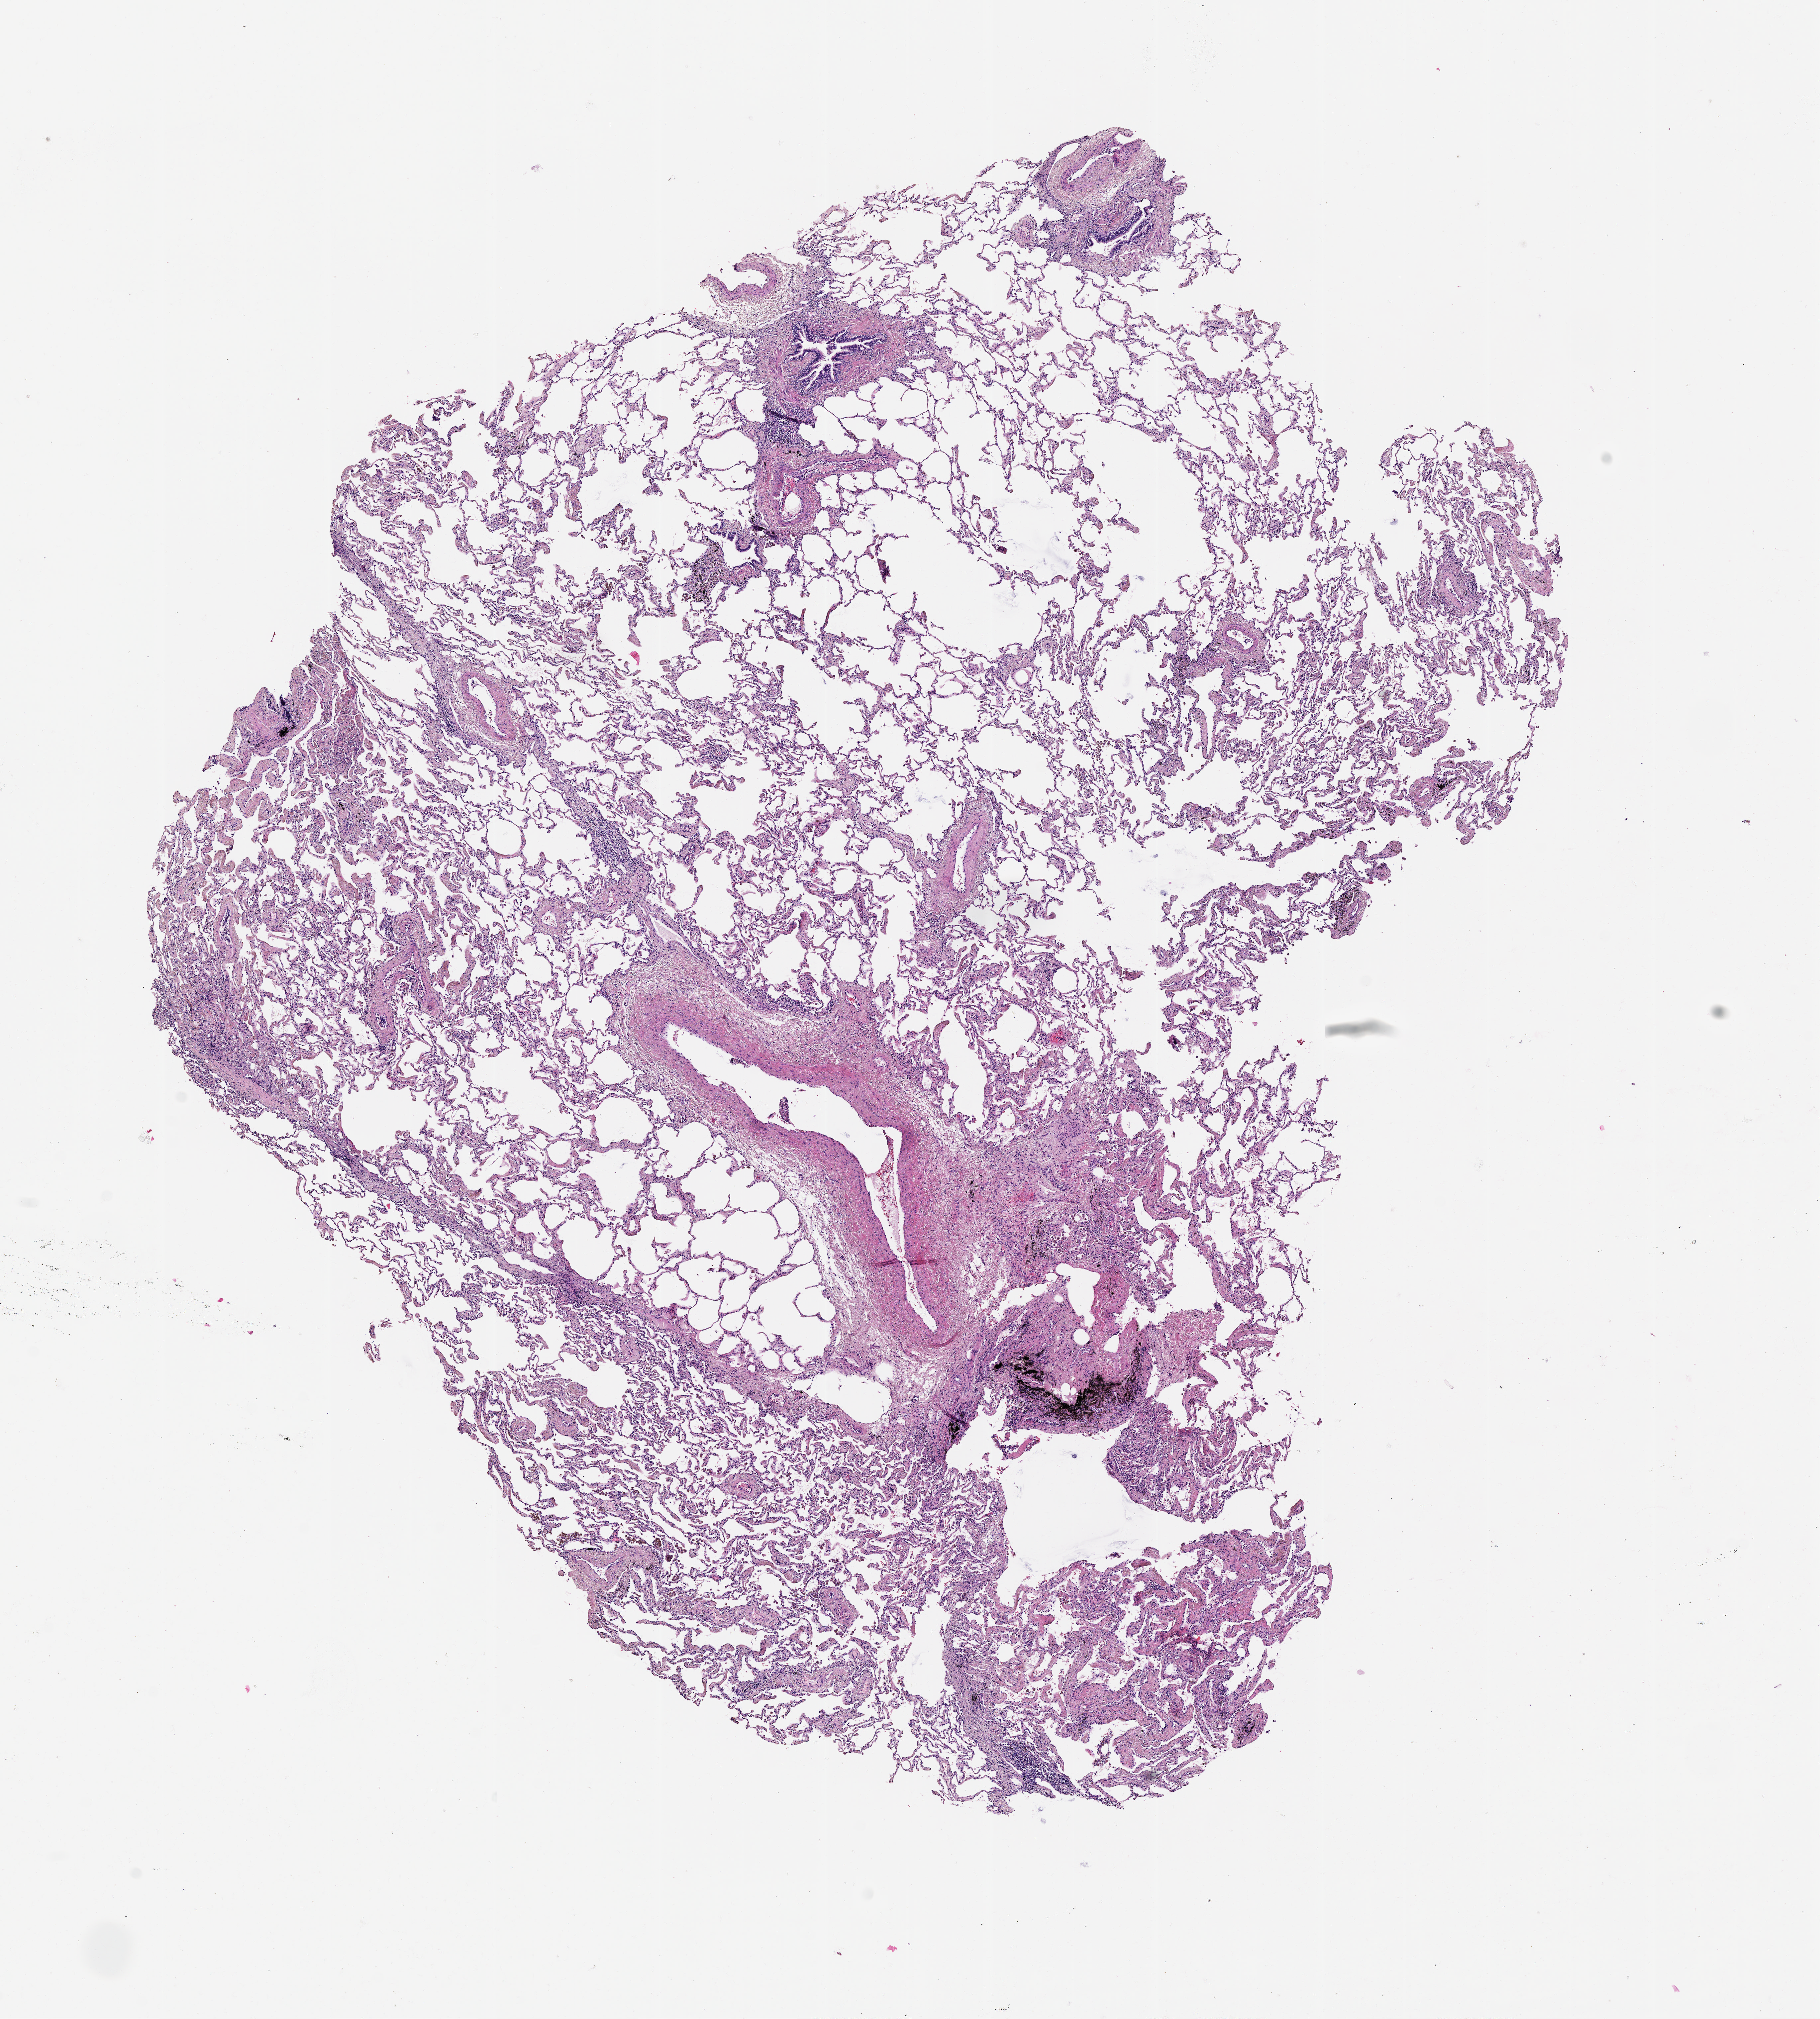
Whole-slide histology image, Hematoxylin and eosin (H&E) stained — low-resolution overview of the scanned area, about 11.0 x 12.2 mm. Lung, tissue type not recorded.
Patient diagnosis (cohort enrolment): squamous cell carcinoma (lung).